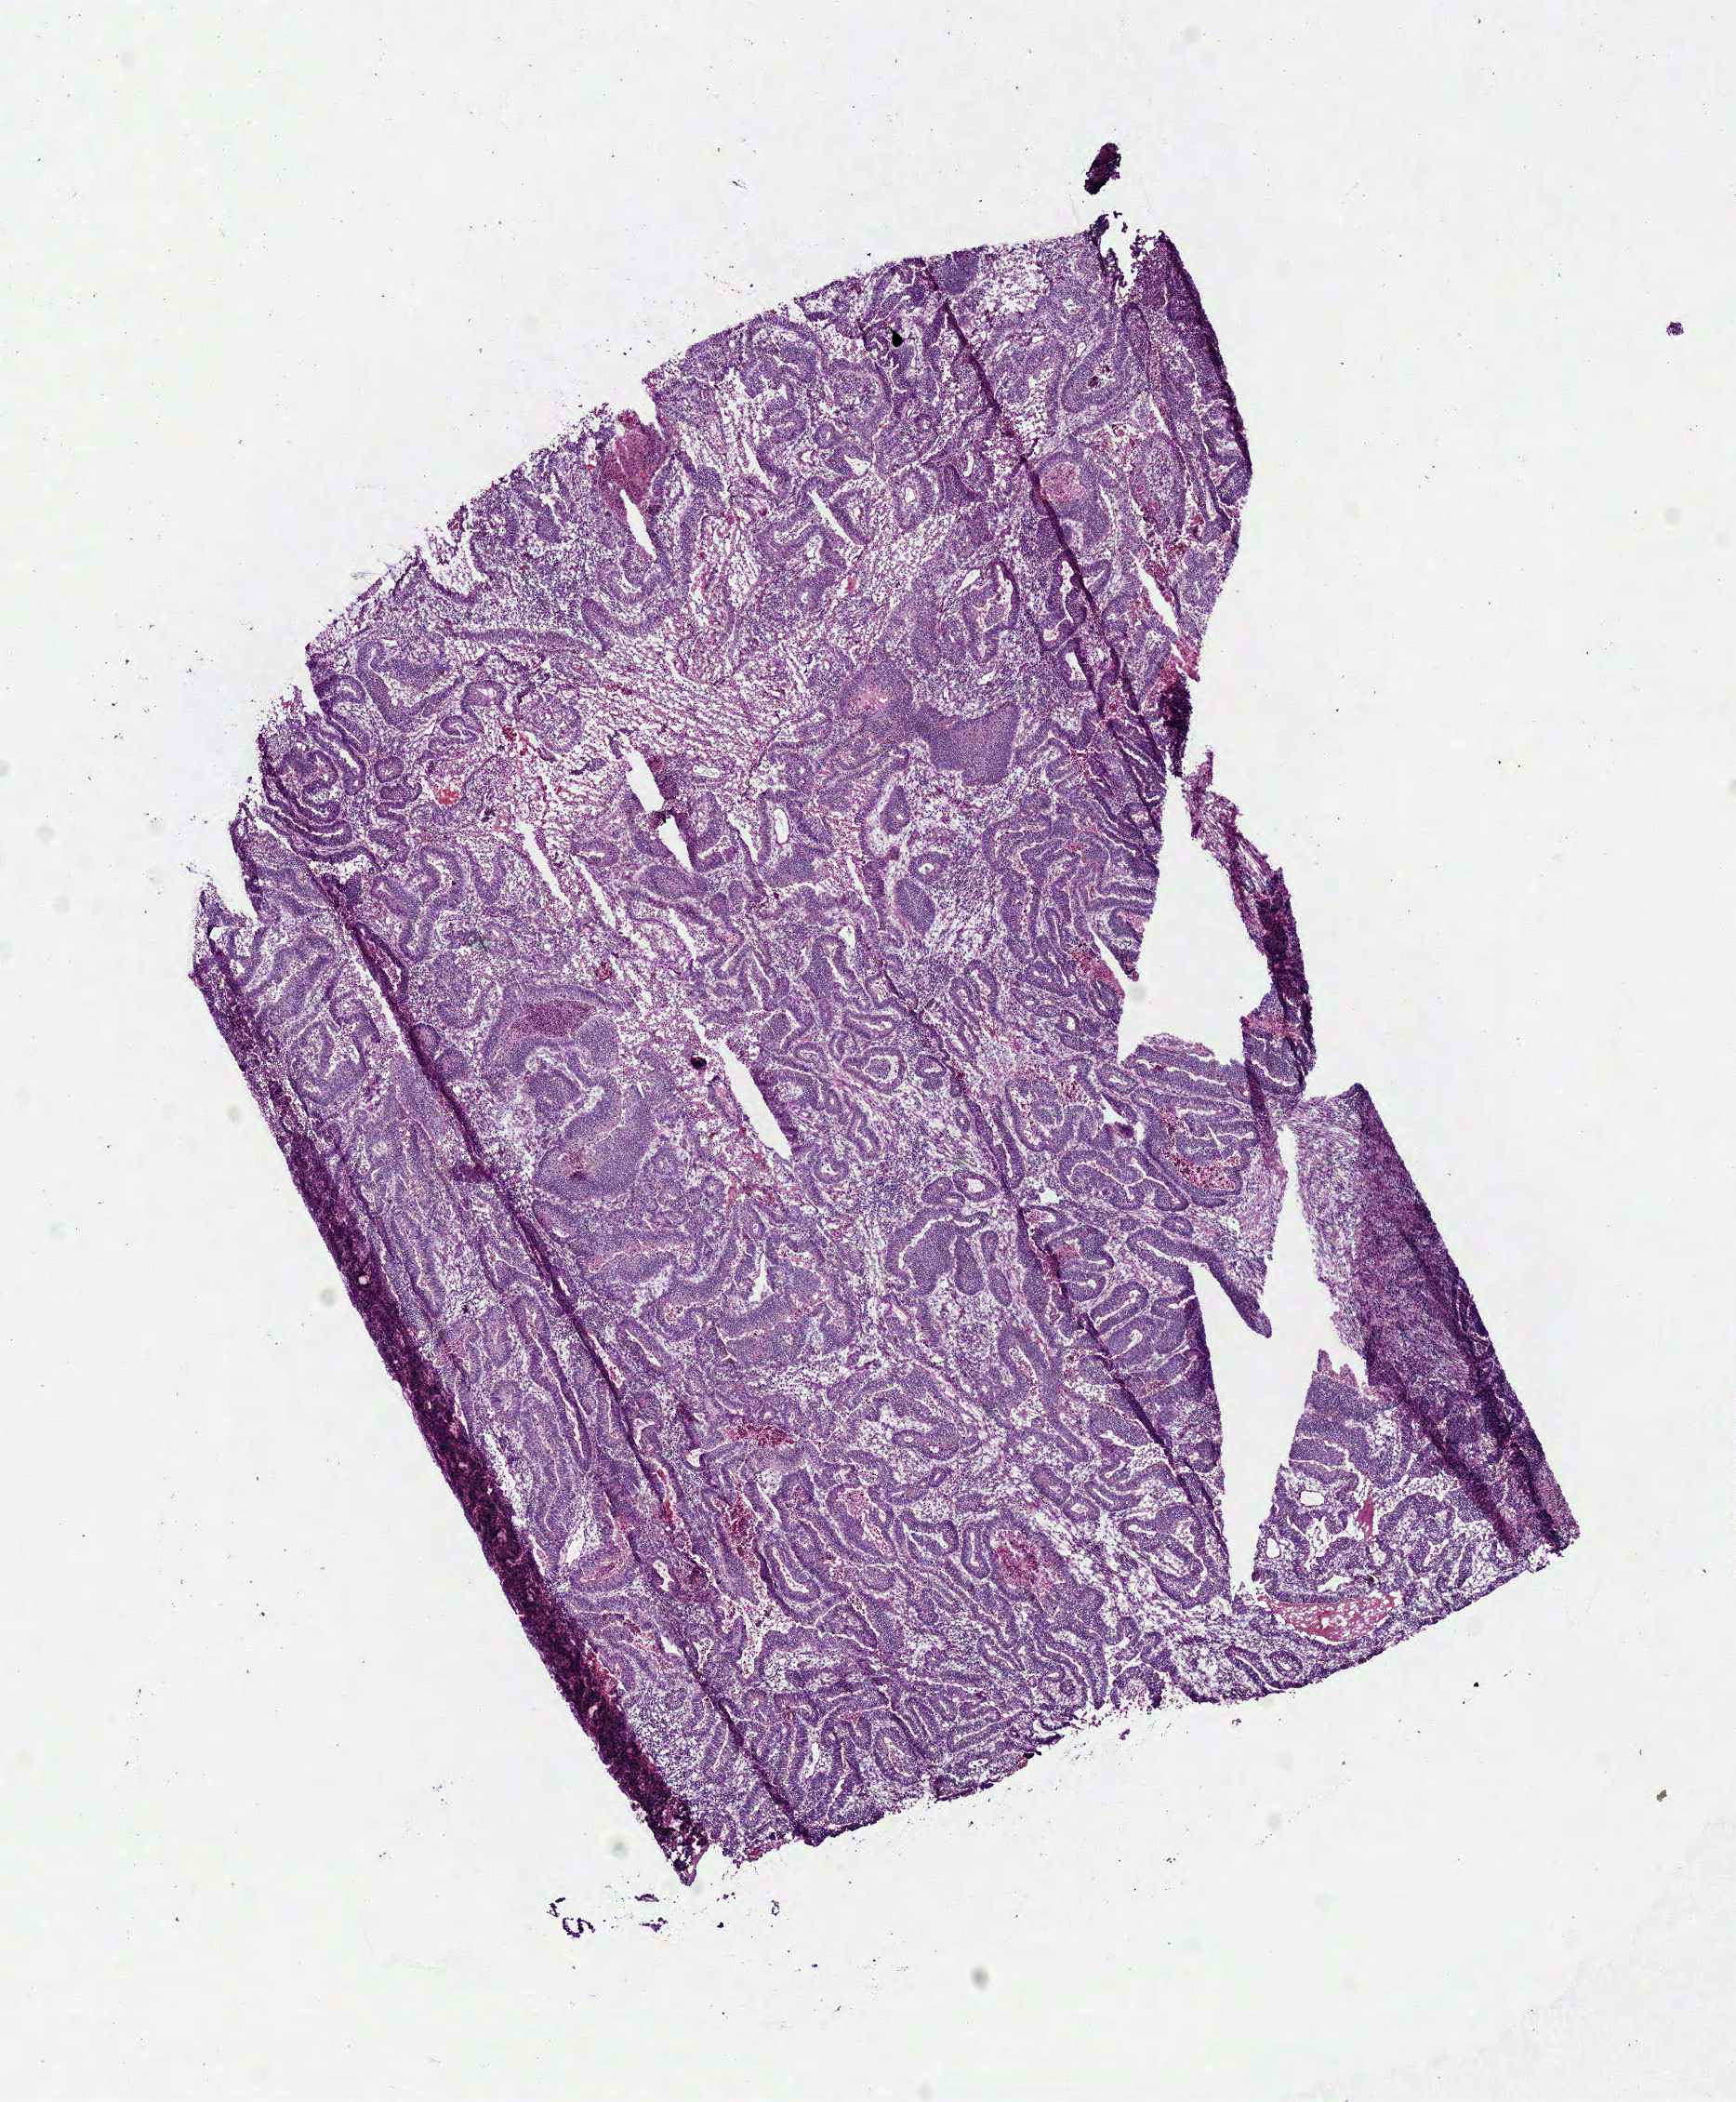
H&E whole-slide image, a low-resolution overview of the entire scanned area, about 7.3 x 8.9 mm; frozen section from the bottom of the tissue portion; primary tumour sample from the rectum. Male patient; age at initial diagnosis 52 years. Composition of this section per pathologist review: tumour cells 77%, tumour nuclei 75%, normal cells 0%, stromal cells 15%, necrosis 8%.
Histologic diagnosis: Adenocarcinoma in tubulovillous adenoma. AJCC pathologic stage: IIIB.